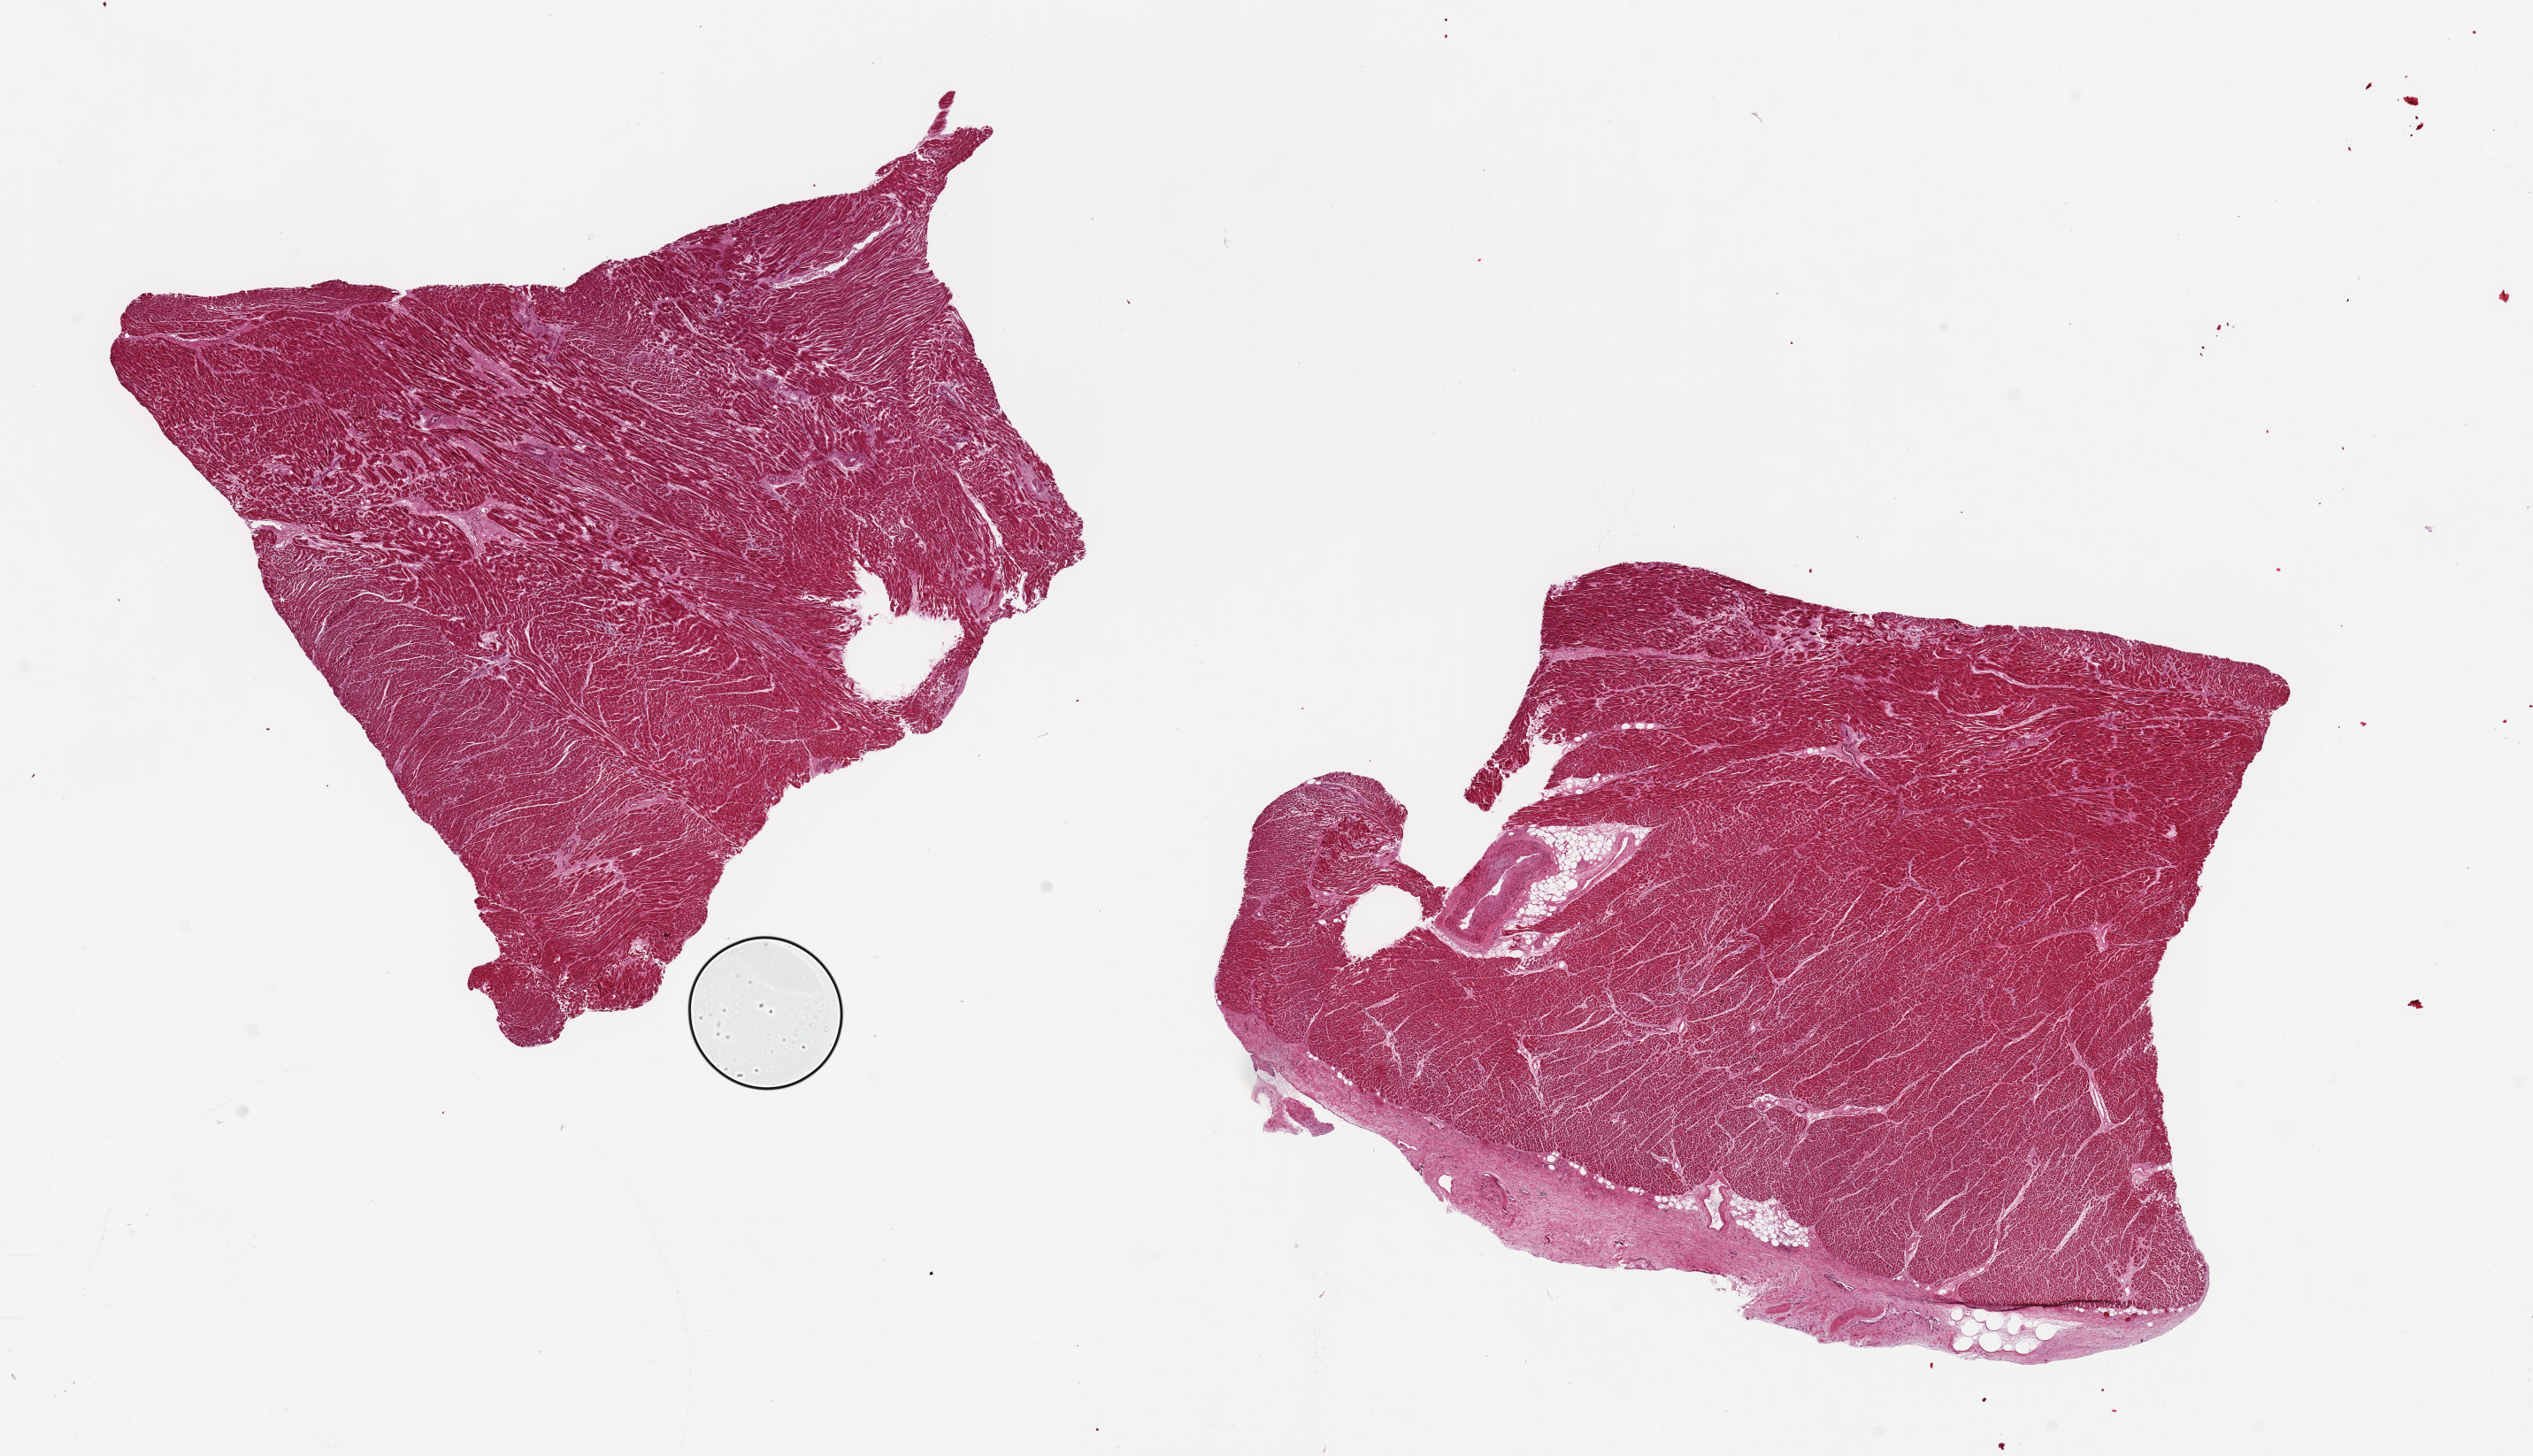
Whole-slide image, H&E stain, shown as a low-resolution overview of the whole scanned area (about 22.6 x 13.0 mm, acquisition: 20x scan), PAXgene-fixed paraffin-embedded (PFPE) section, target tissue: heart, tissue donor sample. Donor: male.
* pathologist's review note for this sample: 2 pieces, 8x8 & 9x6.5mm; 1 with 1mm thick pericardium possibly related to history of coronary bypass surgery)